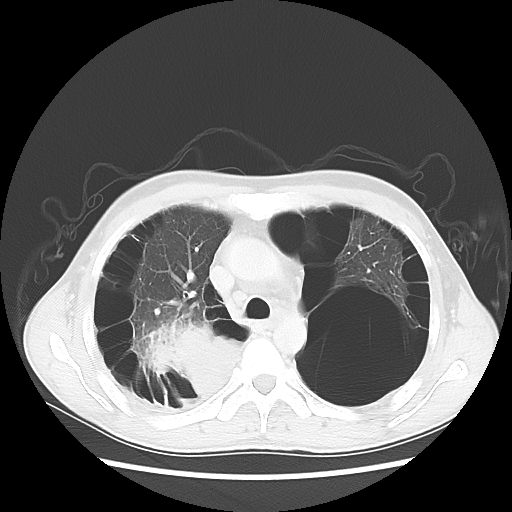
Chest CT, one axial slice. Slice 39 of 57 in the series (ordered by position). Reconstruction kernel LUNG. 140 kVp. Lung window (W 1500 / L -600 HU). 5 mm slice thickness. 512 × 512 image matrix, field of view 351 × 351 mm. Male patient, age 41 years. From the clinical record (not read from this slice): clinical TNM (as recorded): T4 N0 M1a.
Structures marked on this image (rectangle marked by the reading radiologist):
- lung tumour (recorded histology: large cell carcinoma): bounding box (x1, y1, x2, y2) in pixels: (146, 318, 250, 402)